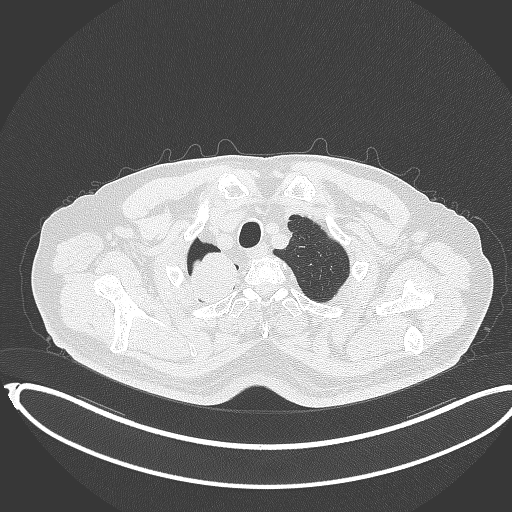
Chest CT, one axial slice; position 334 of 403 along the scan axis; reconstruction kernel B70f; lung window (W 1500 / L -600 HU); 1 mm slice thickness; 512 × 512 image matrix, field of view 436 × 436 mm. Male patient, age 68 years. From the clinical record (not read from this slice): clinical TNM (as recorded): T2a N0 M0.
Annotated regions visible in this slice (rectangle marked by the reading radiologist):
- lung tumour (recorded histology: adenocarcinoma): bounding box (x1, y1, x2, y2) in pixels: (184, 247, 249, 308)